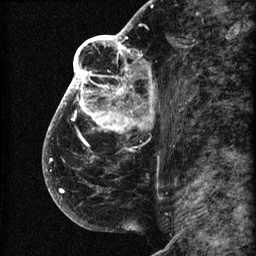
Breast MRI (dynamic contrast-enhanced), one sagittal slice. Slice 40 of 60 in the series (ordered by position). 3 images stored at this slice position (order not interpretable as contrast timing). 1.5 T. TE 4.2 ms, TR 22.7 ms. 256 × 256 image matrix. Female patient, age 48 years. From the clinical record (not read from this slice): setting: breast cancer imaged before/during neoadjuvant chemotherapy; receptor status: triple-negative.
Structures marked on this image (semi-automatic segmentation, software-assisted and operator-edited):
- analysis volume of interest (the breast-tissue region the enhancement analysis was run in; not a lesion): bounding box [x1, y1, x2, y2] px = [44, 30, 173, 207]
- tumour enhancement mask (voxels above the 90 % enhancement threshold inside the analysis volume of interest): [44, 30, 153, 193]